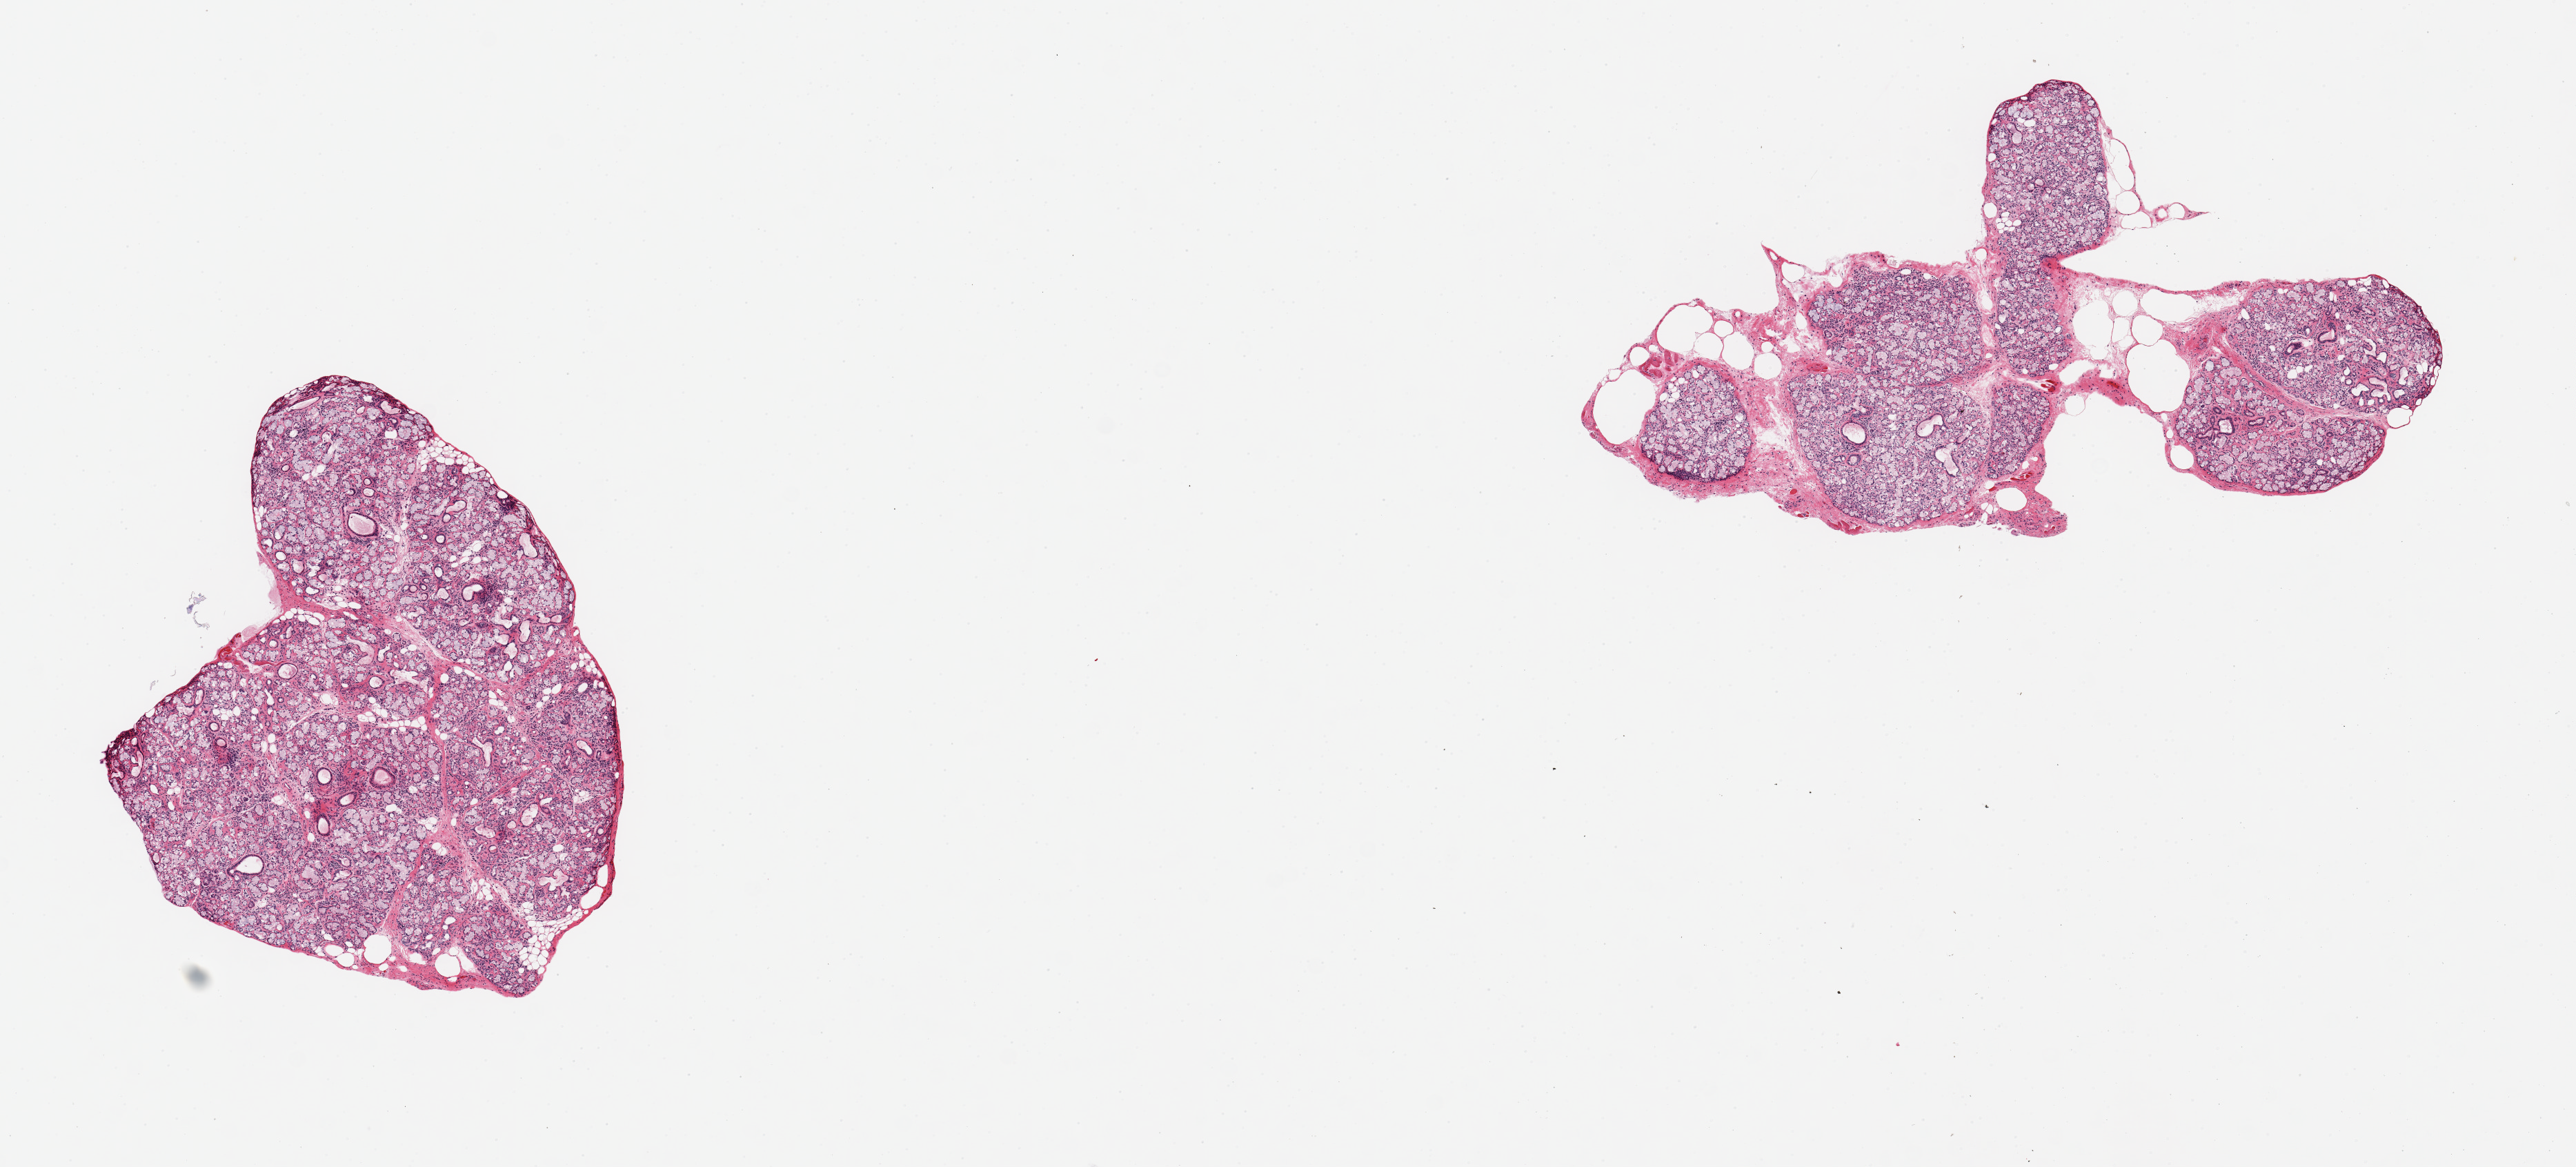
Digitized hematoxylin and eosin (H&E)-stained section, brightfield, shown as a low-resolution overview of the whole scanned area (about 14.8 x 6.7 mm); PAXgene-fixed paraffin-embedded (PFPE) section; section of minor salivary gland (target tissue); tissue donor sample. Donor: male.
Review note (as recorded): 2 pieces, 90% glandular elements; ~10% fat.